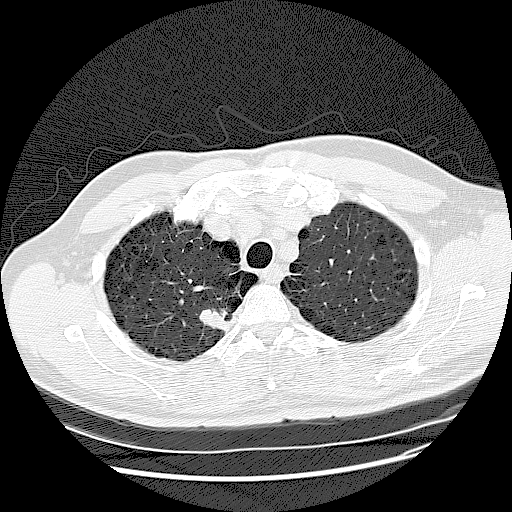
Low-dose screening chest CT, one axial slice. Position 108 of 132 along the scan axis. Reconstruction kernel LUNG. 120 kVp. Lung window (W 1500 / L -600 HU). 512 × 512 image matrix.
Structures marked on this image (manually delineated by an expert):
- lesion 1 (tumor, upper lobe of right lung): bounding box <199,308,230,331> (left, top, right, bottom; pixels)